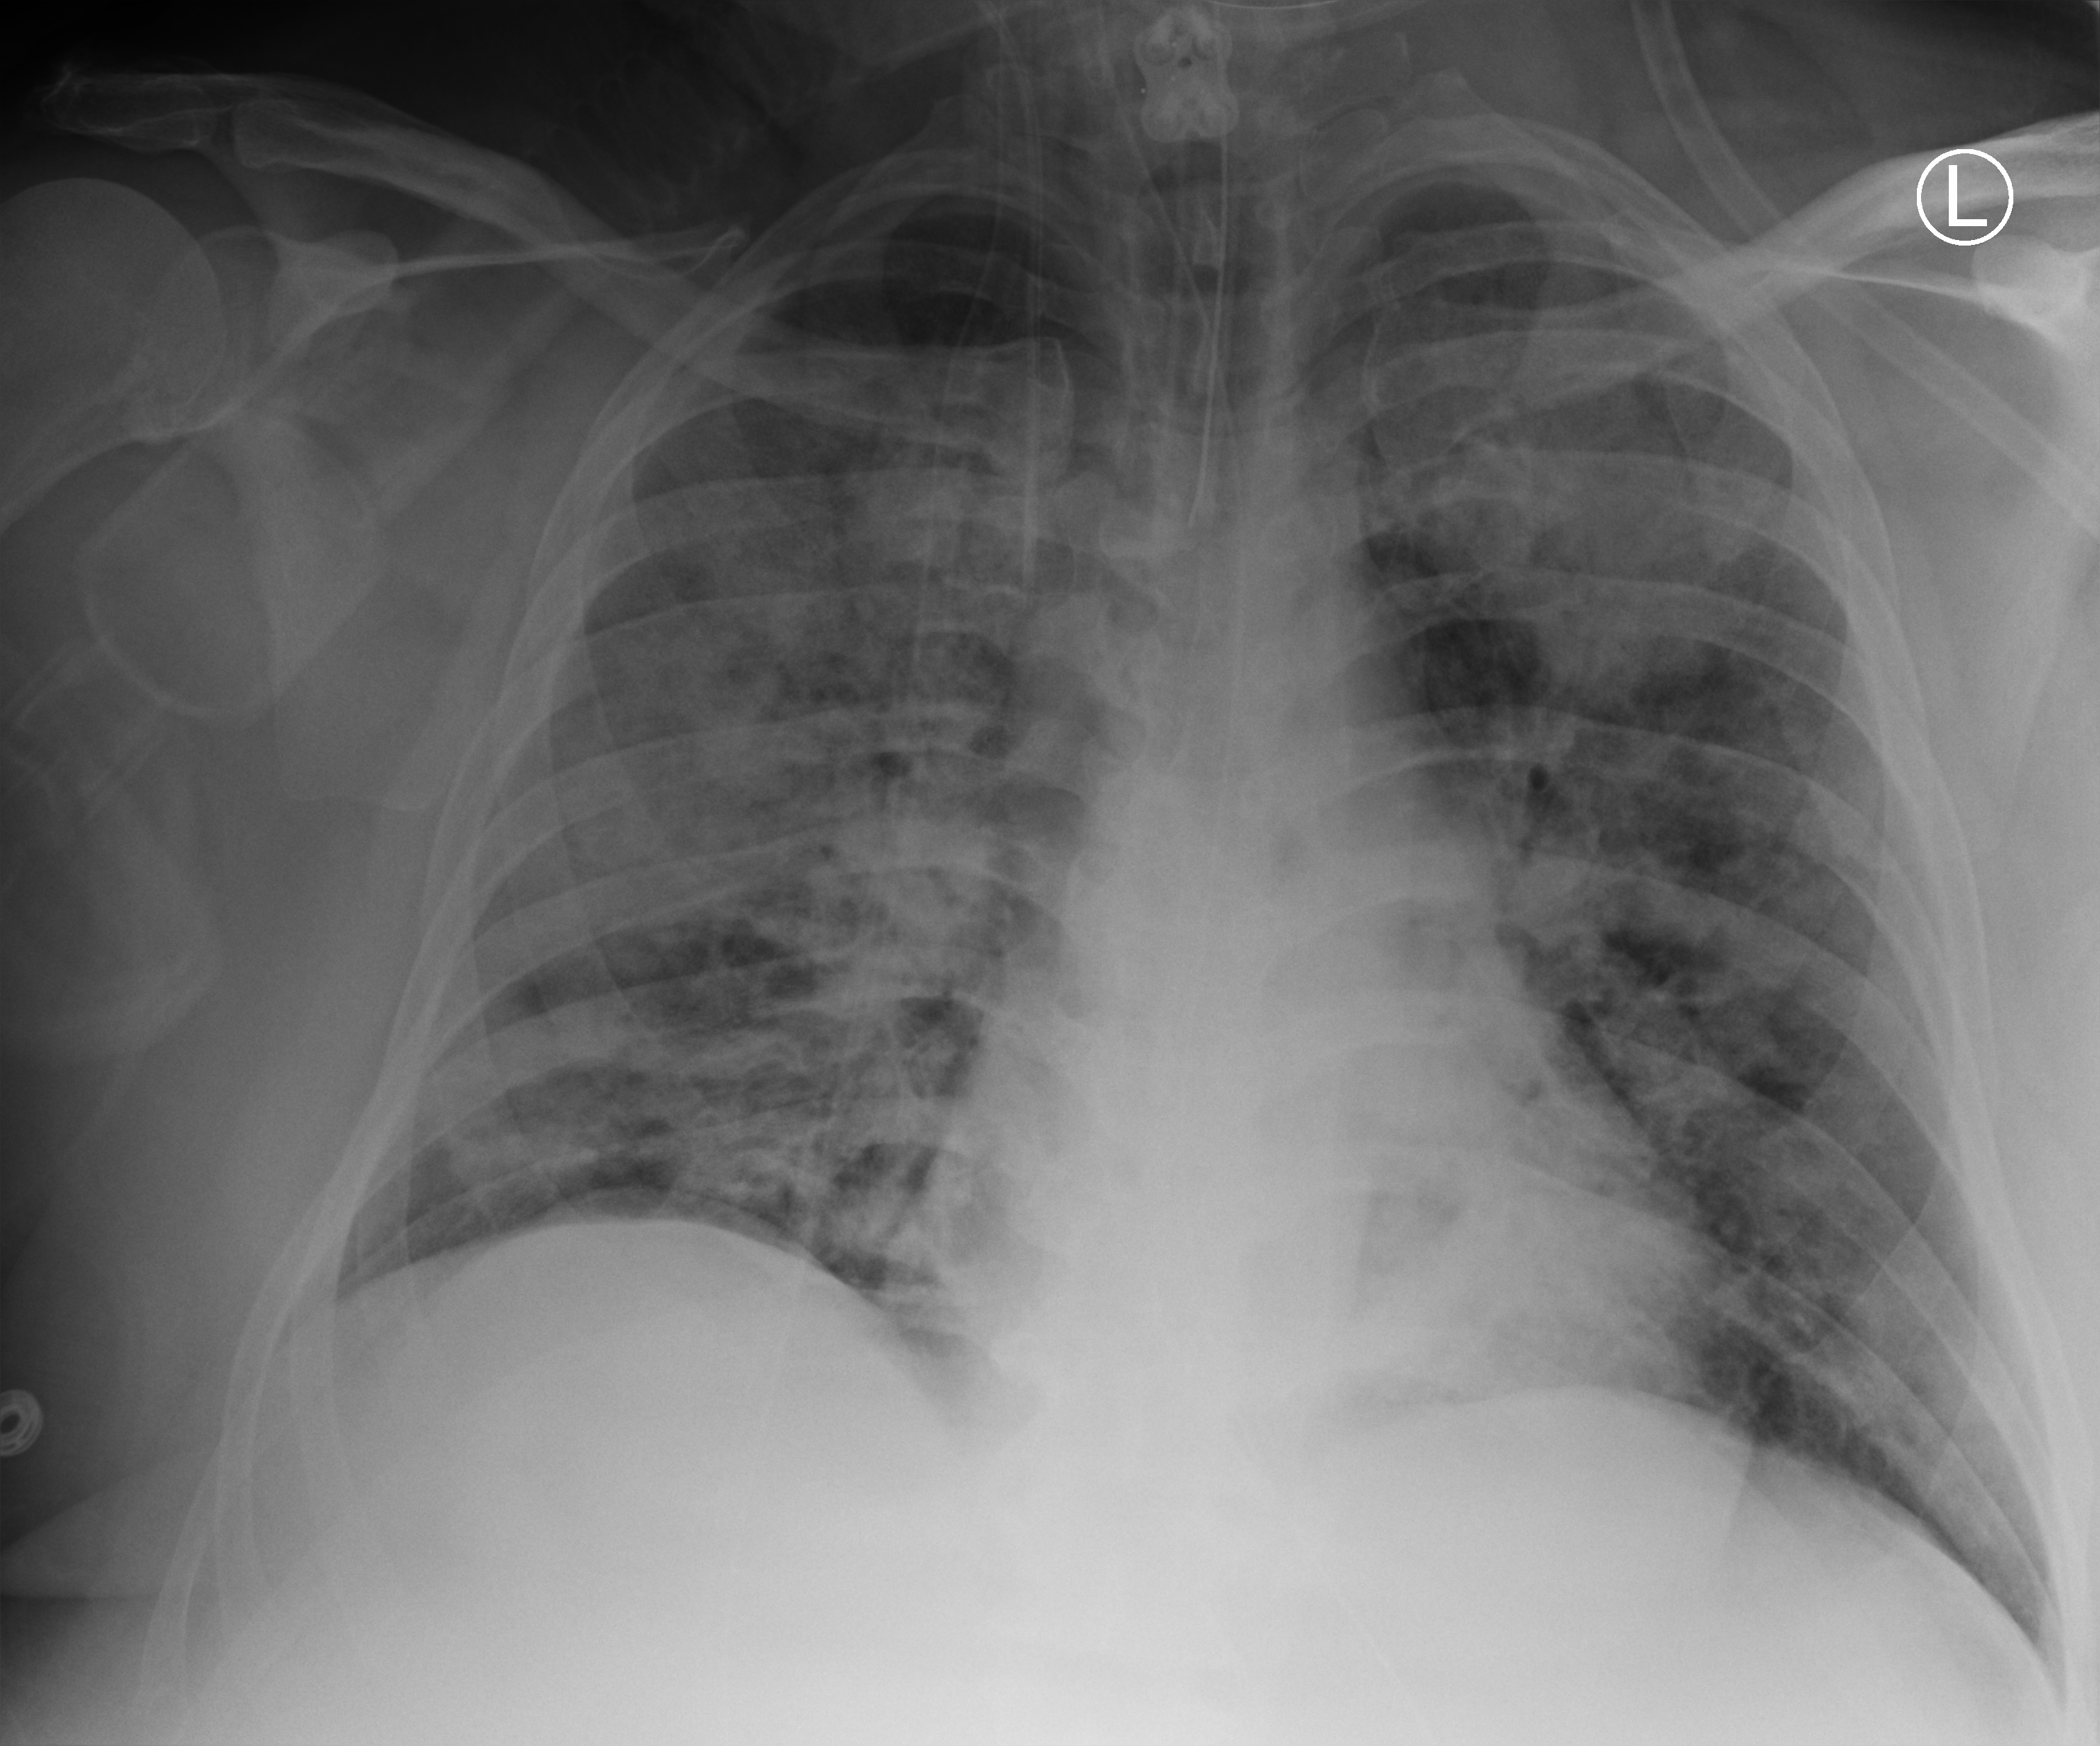
Portable chest radiograph, anteroposterior (AP) projection. Patient hospitalised with COVID-19; male, aged 18–59 years.
From the hospital-stay record, not from the radiograph (when in the stay this image was taken is not recorded):
- chronic kidney disease (admission record): no
- hypertension (admission record): yes
- smoking status (admission record): never